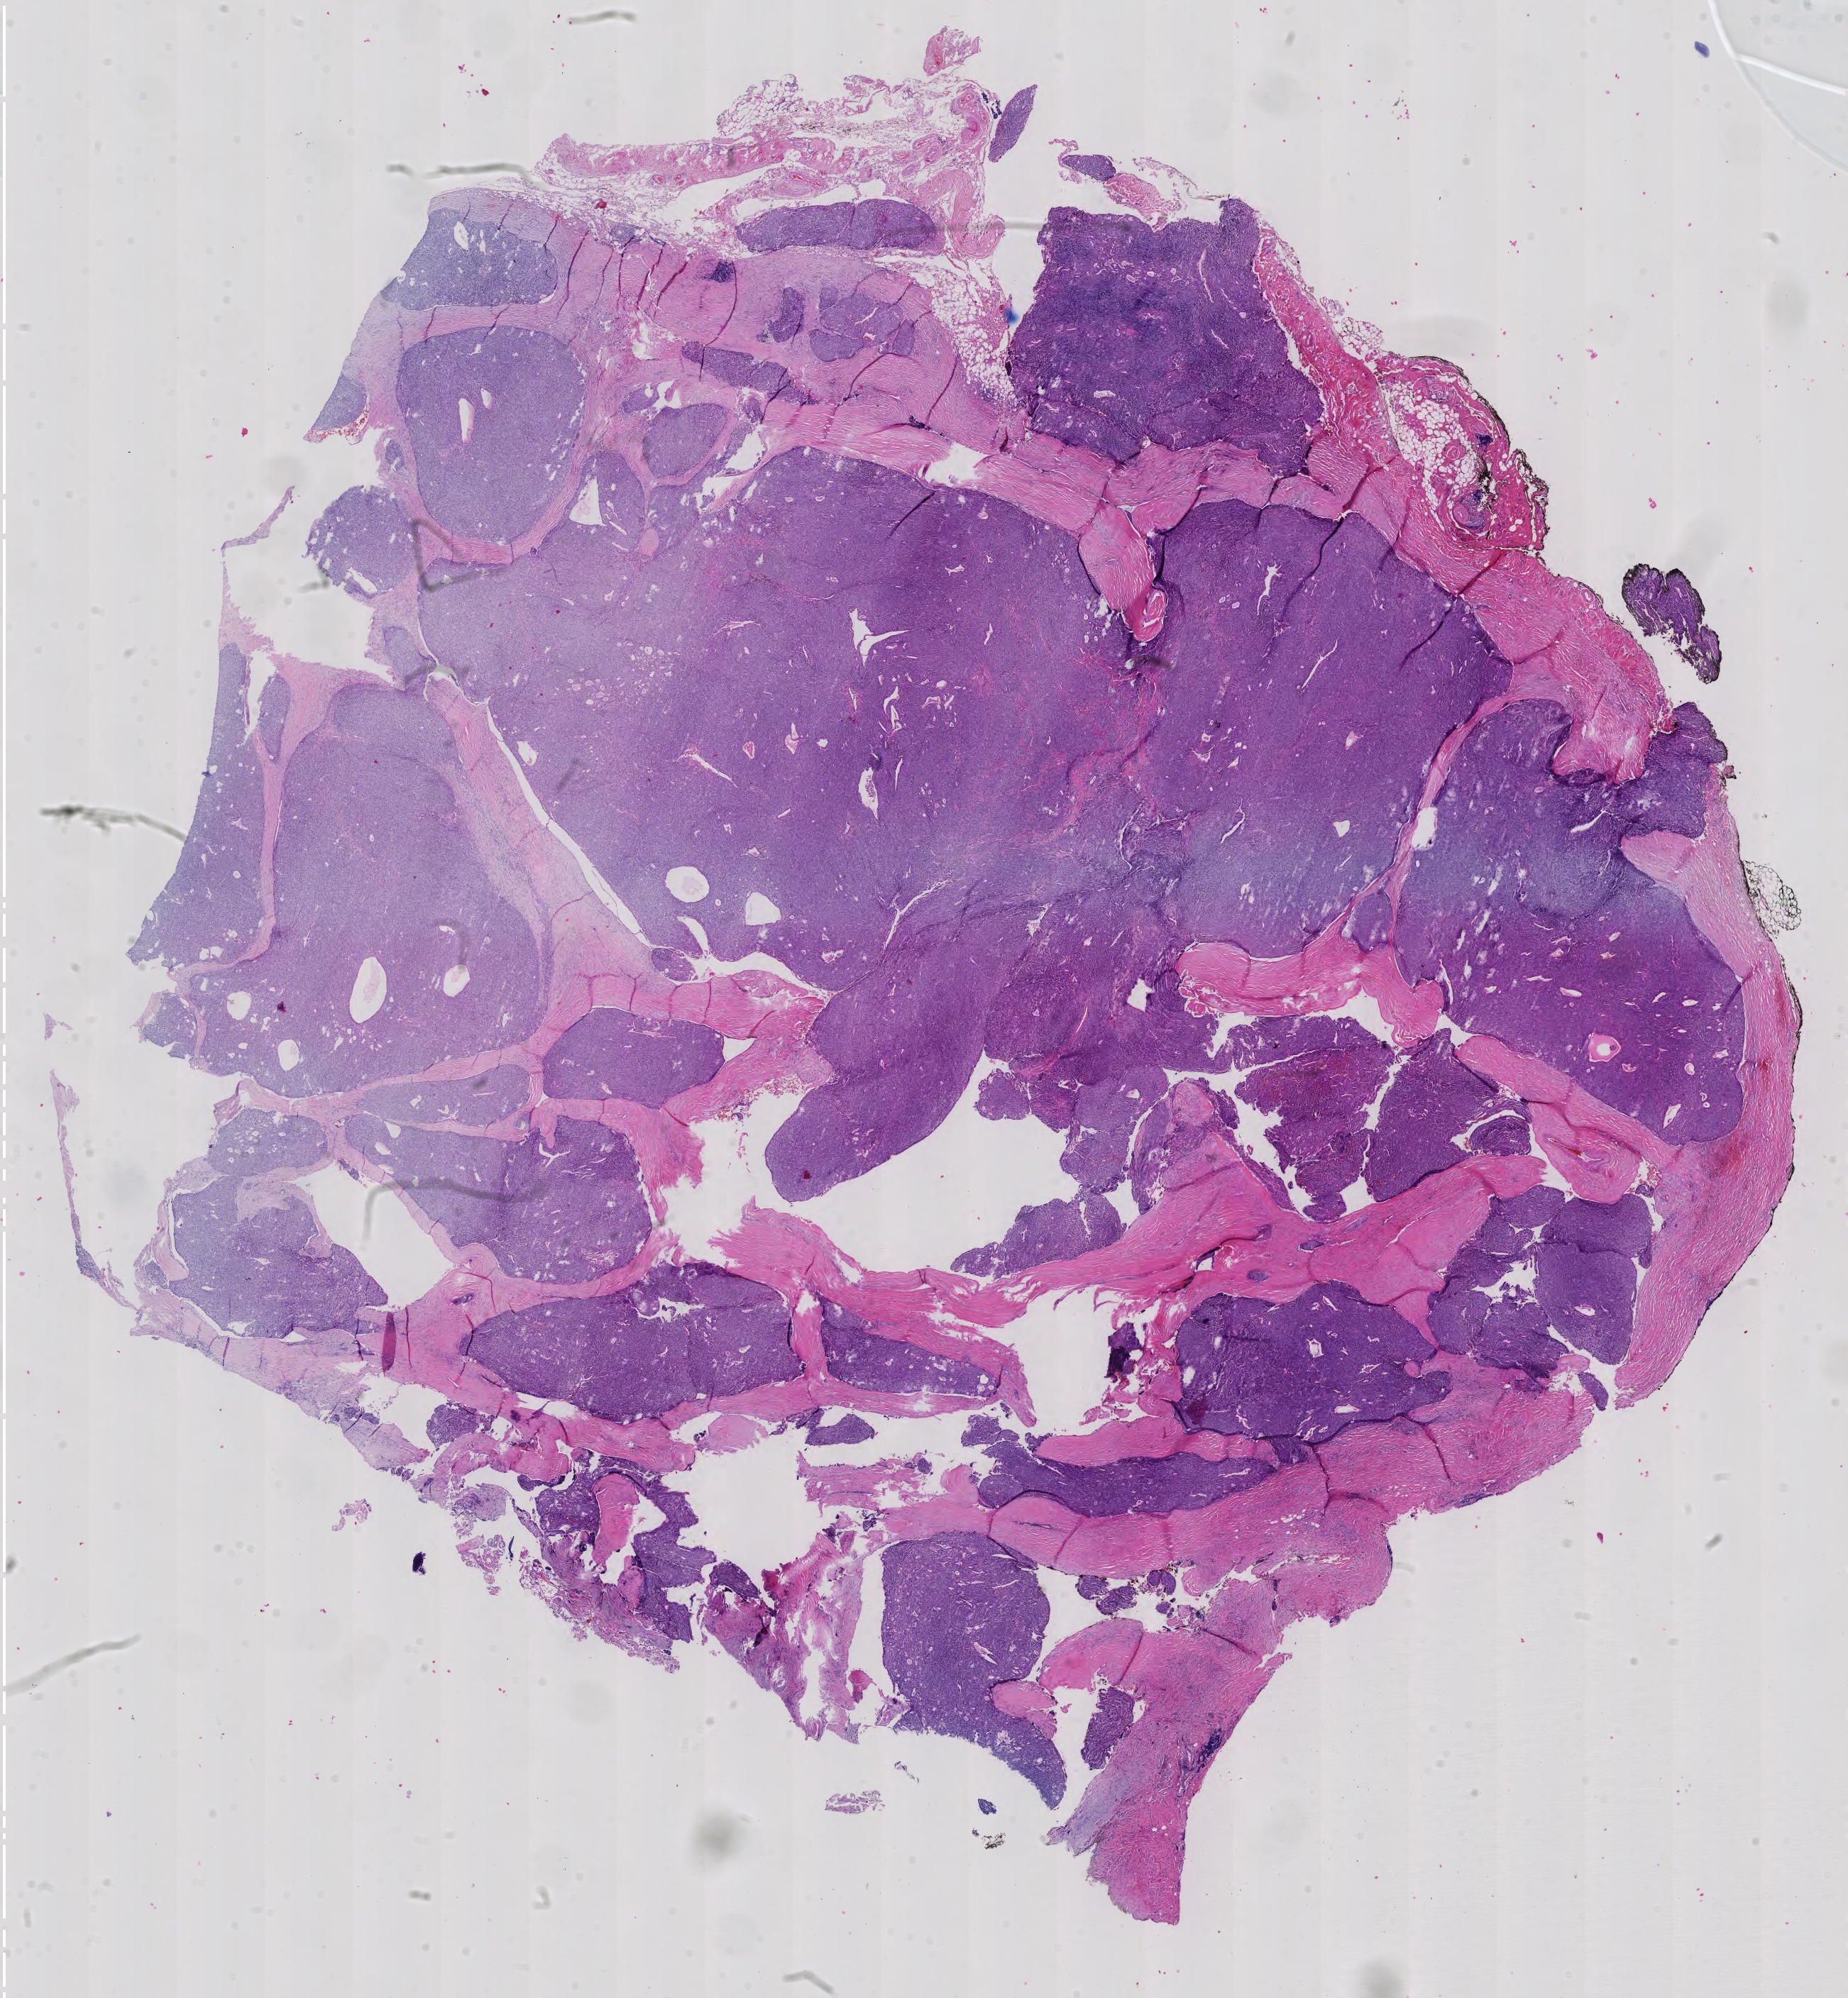
Whole-slide histology image, H&E-stained, shown as a low-resolution overview of the whole scanned area (about 19.0 x 20.5 mm), FFPE section, primary tumour sample from the thymus. Male, age 73 years at initial diagnosis.
Pathologic diagnosis: Thymoma, type A, malignant.